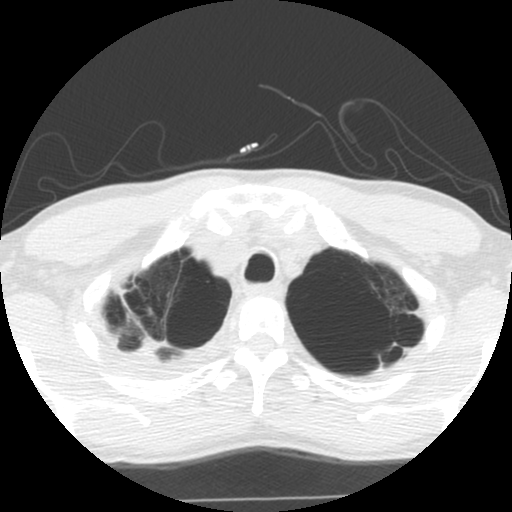
Low-dose screening chest CT, one axial slice; position 101 of 119 along the scan axis; lung window (W 1500 / L -600 HU); 2.5 mm slice thickness; 512 × 512 image matrix, field of view 295 × 295 mm.
Structures marked on this image (outlined manually by an expert reader):
- lesion 1 (tumor, upper lobe of right lung): box from (x=135, y=337) to (x=163, y=360) px